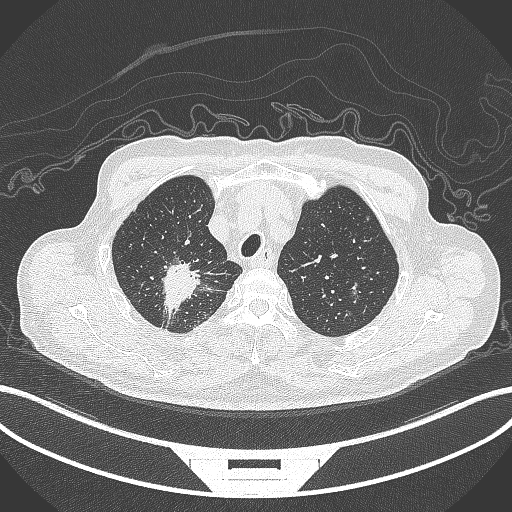
Chest CT, one axial slice; position 313 of 407 along the scan axis; lung window (W 1500 / L -600 HU); 1 mm slice thickness; 512 × 512 image matrix, field of view 400 × 400 mm. Patient: male, 69 years. From the clinical record (not read from this slice): clinical TNM (as recorded): T1c N1 M1.
Outlined on this slice (rectangle marked by the reading radiologist):
- lung tumour (recorded histology: adenocarcinoma): bounding box <158,258,206,314> (left, top, right, bottom; pixels)